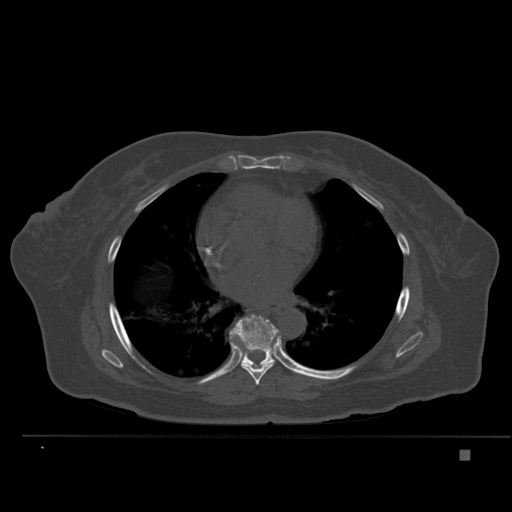
CT including the spine, one axial slice; position 320 of 477 along the scan axis; bone window (W 1800 / L 400 HU); 1.5 mm slice thickness; 512 × 512 image matrix, field of view 422 × 422 mm. Female patient, age 74 years. Case-level facts recorded for this patient, not image findings: primary cancer: colon.
Structures marked on this image (semi-automatic segmentation, software-assisted and operator-edited):
- T7 vertebra: bounding box [x1, y1, x2, y2] px = [230, 334, 275, 385]
- T8 vertebra: [230, 315, 279, 367]